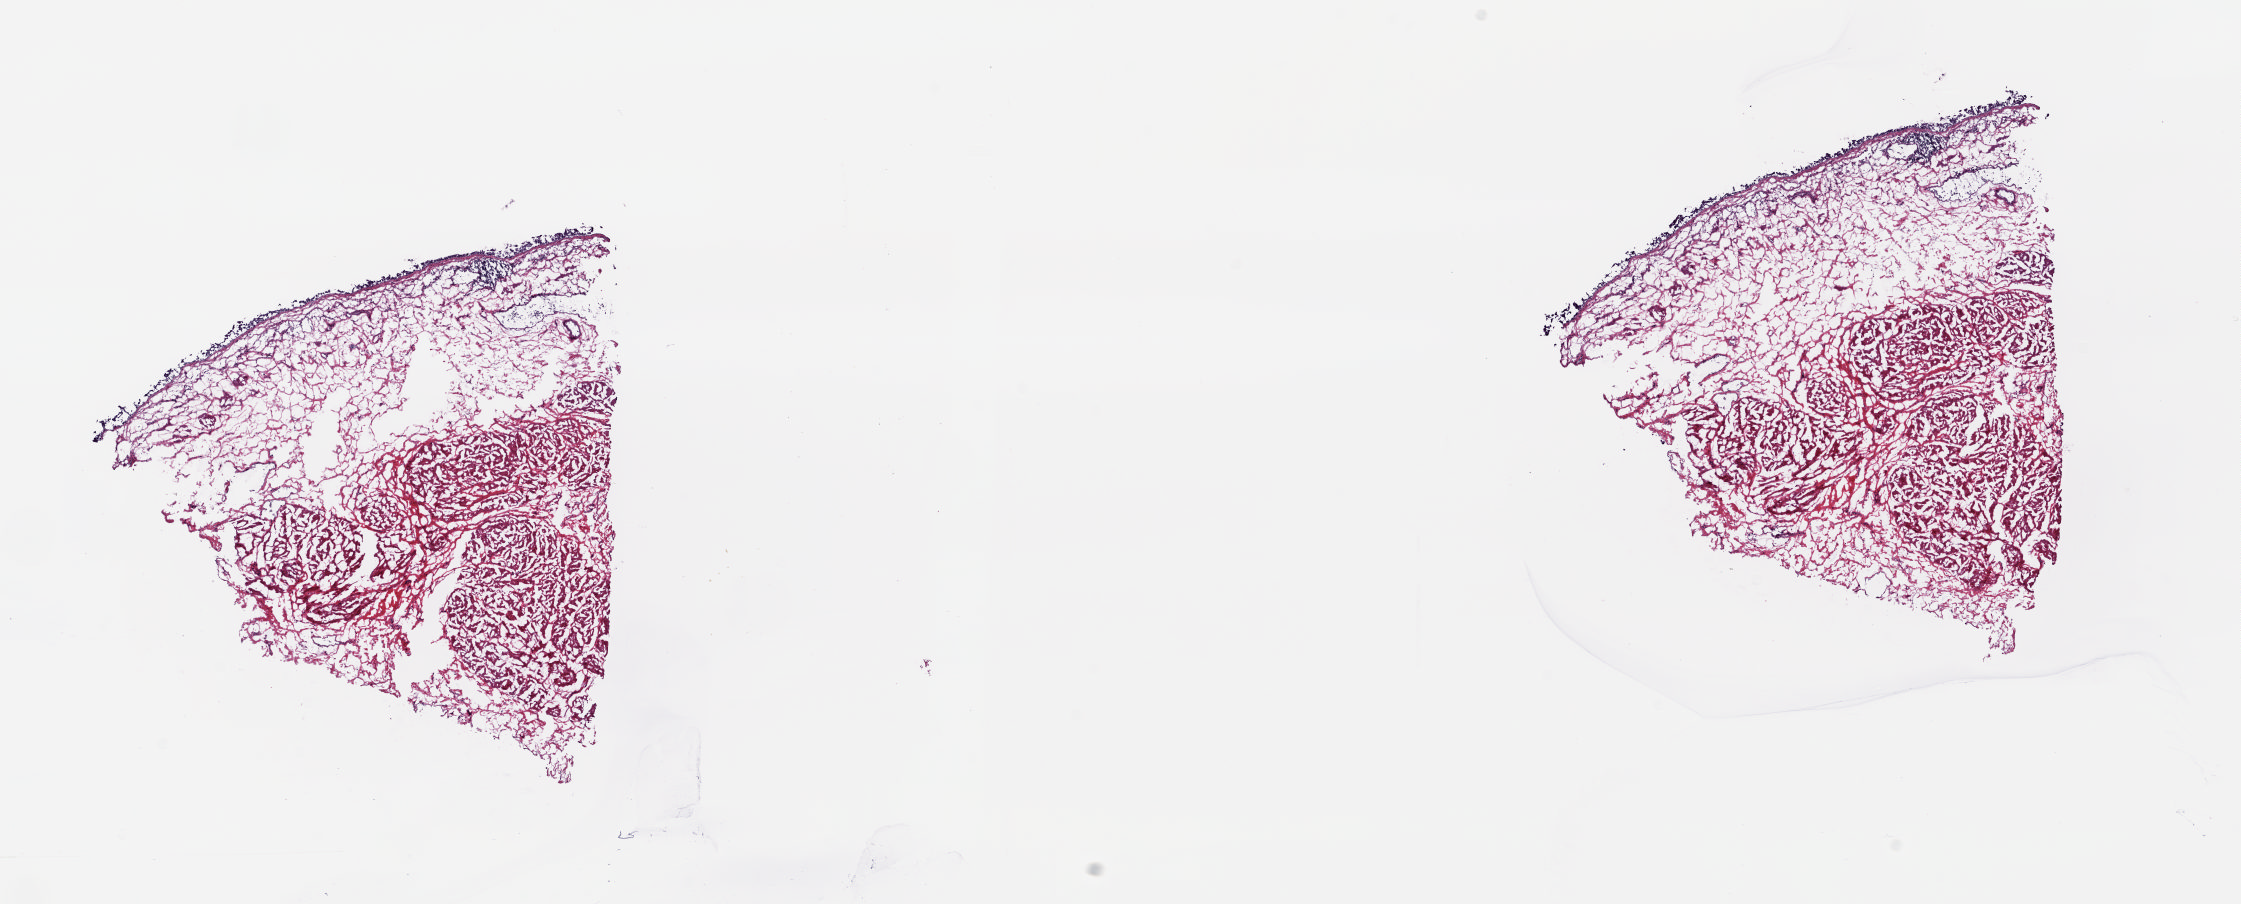
Whole-slide histology image, Hematoxylin and eosin (H&E) stained — a low-resolution overview of the entire scanned area, about 17.8 x 7.2 mm (acquisition: 20x scan). Frozen section from the top of the tissue portion. Bladder, solid tissue normal (non-tumour tissue) sample. Patient: male, age at initial diagnosis 75 years. Slide review estimates, as recorded: tumour cells 0%, tumour nuclei 0%, normal cells 100%, stromal cells 0%, necrosis 0%. Inflammatory infiltration, as recorded: lymphocyte infiltration 0%, monocyte infiltration 0%, neutrophil infiltration 0%.
* this section: solid tissue normal sample (biorepository sample class)
* patient diagnosis: Transitional cell carcinoma (posterior wall of bladder)